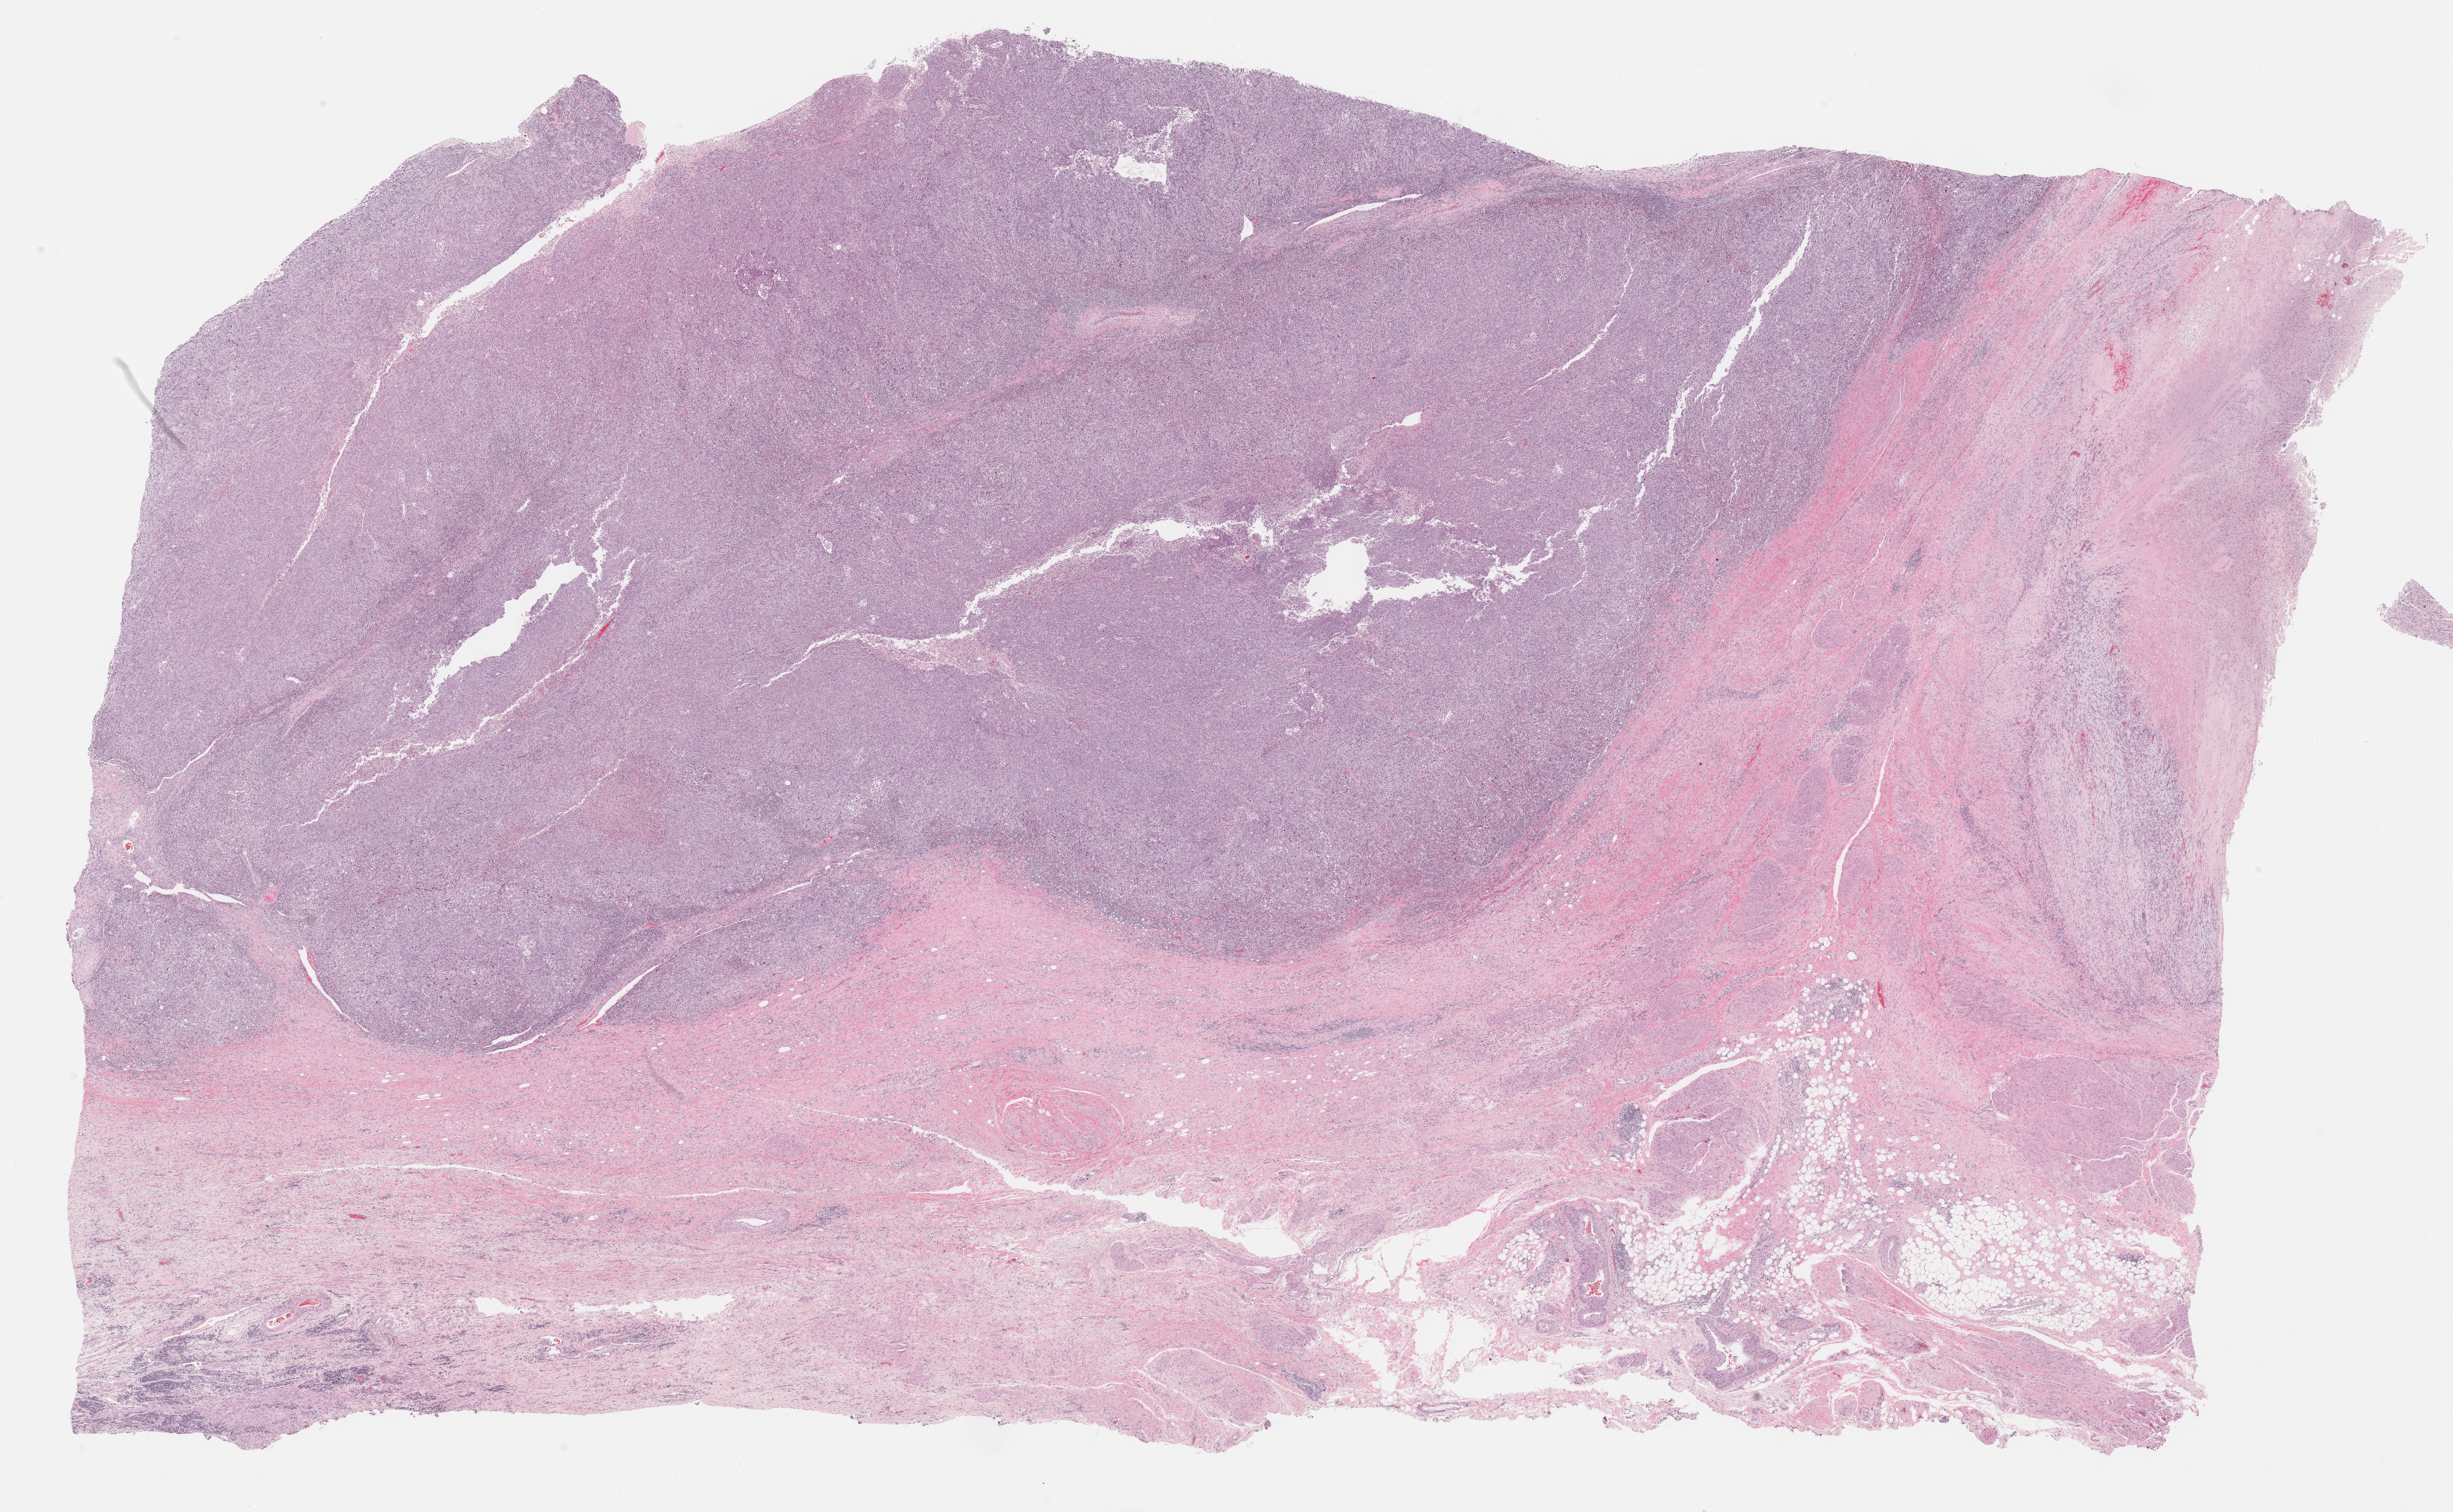
Digitized H&E-stained tissue section (whole slide), whole scanned area (about 26.7 x 16.4 mm, slide scanned at 40x) shown as a low-resolution overview. FFPE section. Bladder, primary tumour sample. Patient: male, age at initial diagnosis 57 years. Histologic grade: high grade.
• pathologic diagnosis: Transitional cell carcinoma (posterior wall of bladder)
• AJCC pathologic stage: III (7th edition)